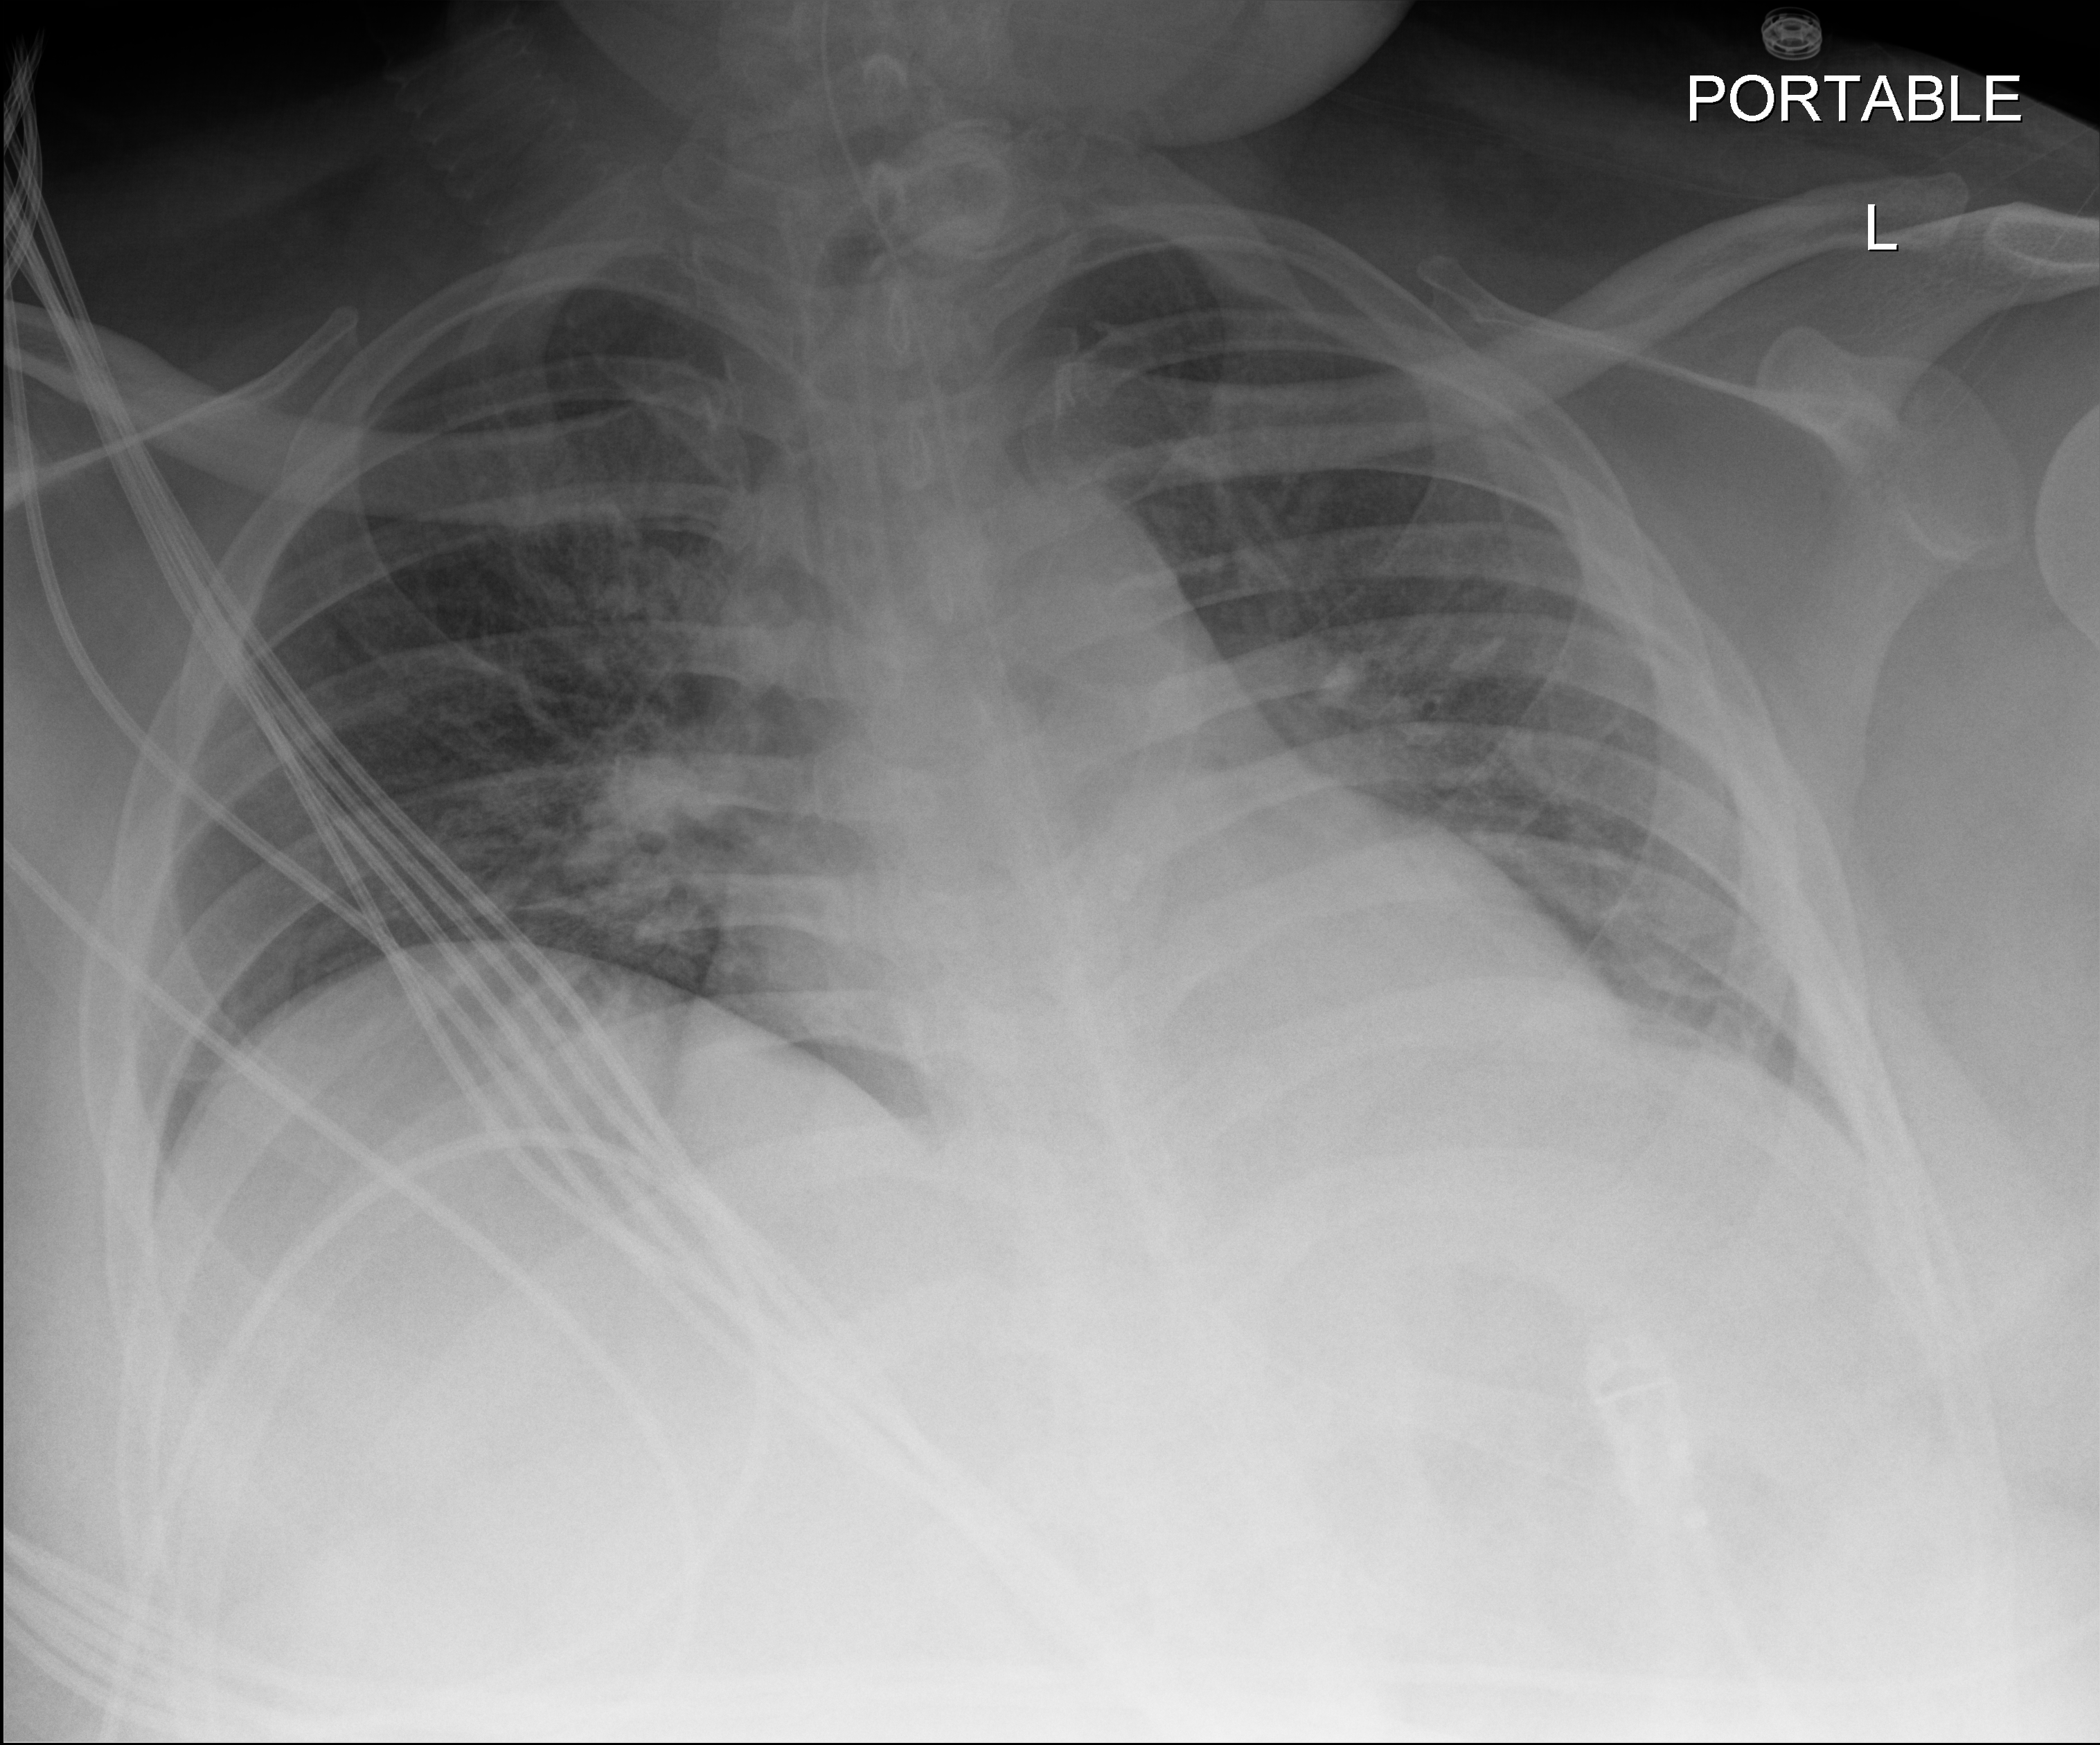
Portable chest radiograph; anteroposterior (AP) projection. Male patient hospitalised with COVID-19, age 18–59 years.
Hospital-stay facts (about this admission, not read from this image; timing relative to this image not recorded): diabetes (admission record): yes; mechanically ventilated during this hospital stay: yes.